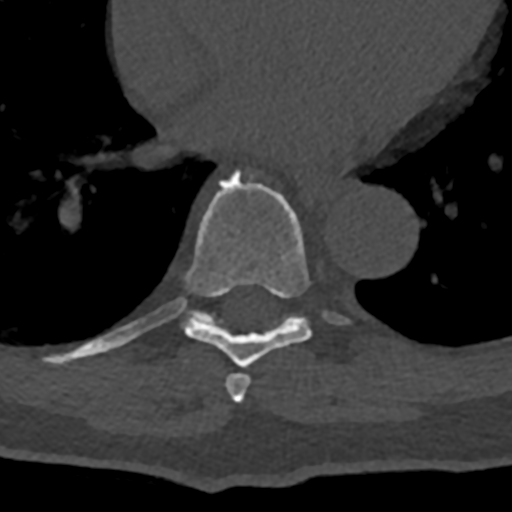
CT including the spine, one axial slice. Slice 702 of 797 in the series (ordered by position). 120 kVp. Bone window (W 1800 / L 400 HU). 0.5 mm slice thickness. 512 × 512 image matrix, field of view 160 × 160 mm. Patient: male, 74 years. From the clinical record (not read from this slice): primary cancer: renal; vertebrae with lytic lesions (as recorded): T10, L1, L2, L3, L4, L5.
Structures marked on this image (semi-automatic segmentation, software-assisted and operator-edited):
- T7 vertebra: bounding box [x1, y1, x2, y2] px = [225, 373, 251, 403]
- T8 vertebra: [70, 170, 350, 368]
- T9 vertebra: [189, 310, 215, 324]